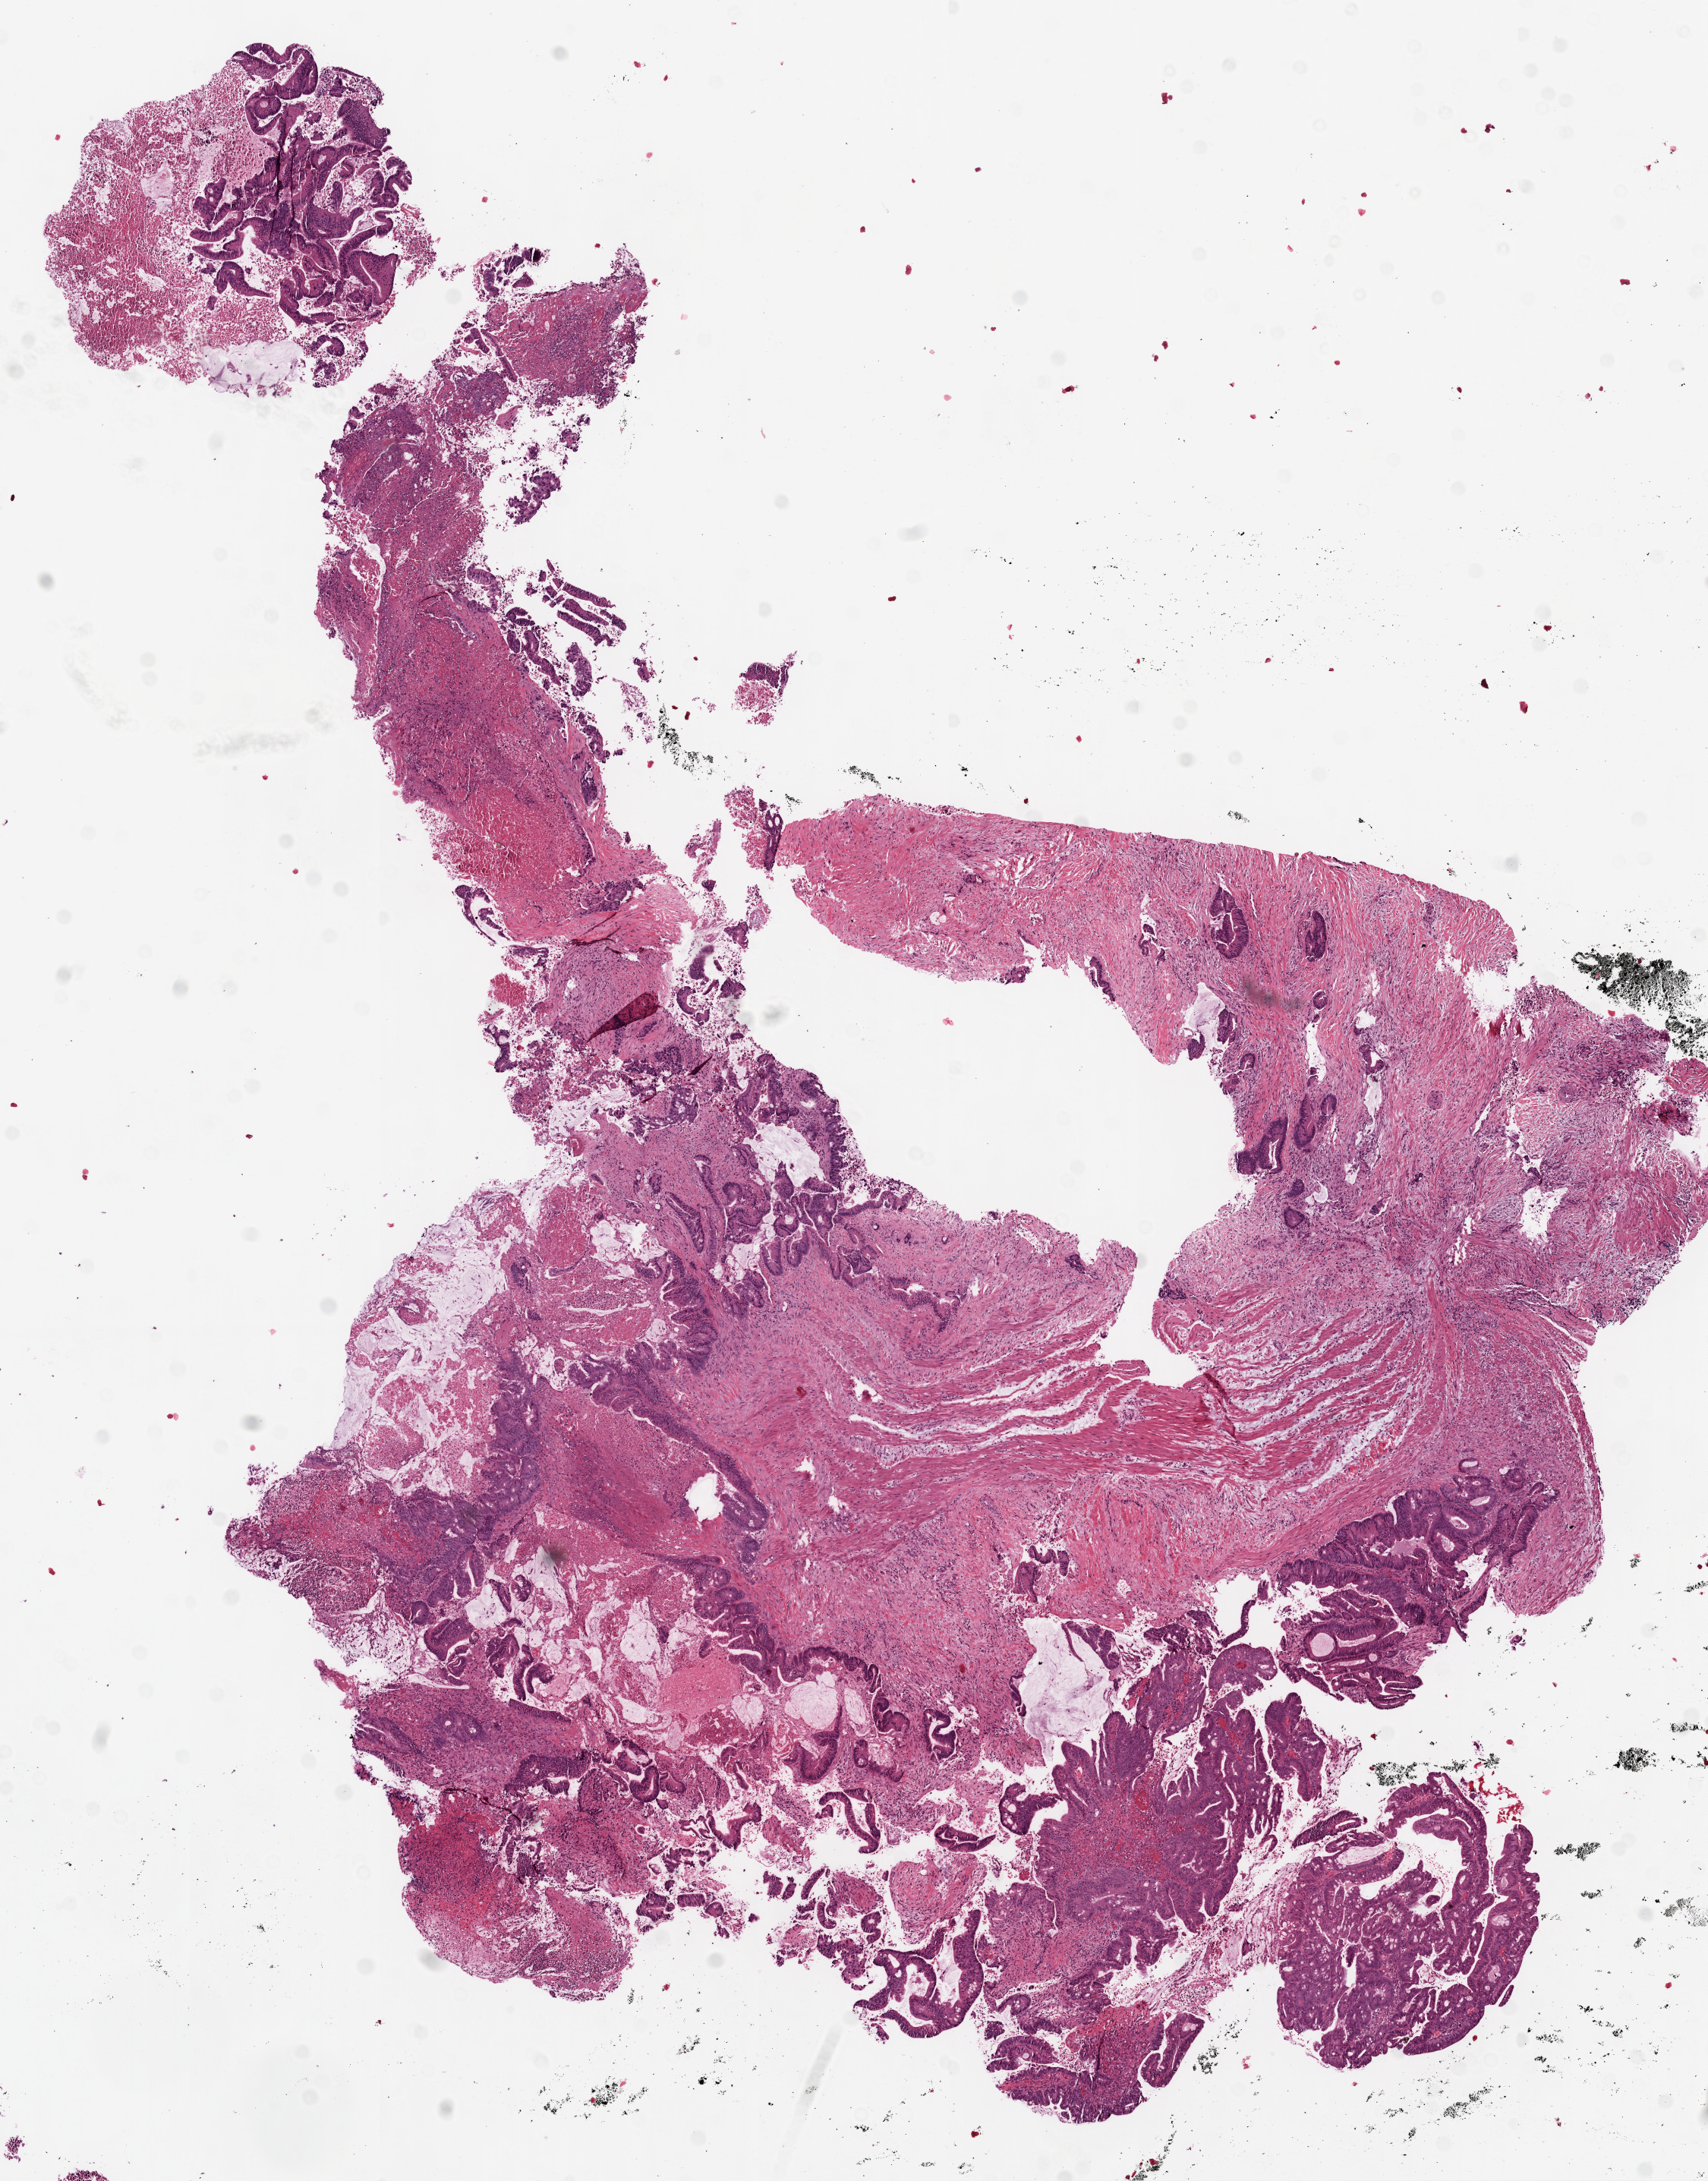
Digitized Hematoxylin and eosin (H&E) stained tissue section (whole slide) — whole scanned area (about 9.0 x 11.5 mm) shown as a low-resolution overview; frozen section from the top of the tissue portion; primary tumour sample from the colon. Male, age 70 years at initial diagnosis.
Diagnosis: Adenocarcinoma, NOS.